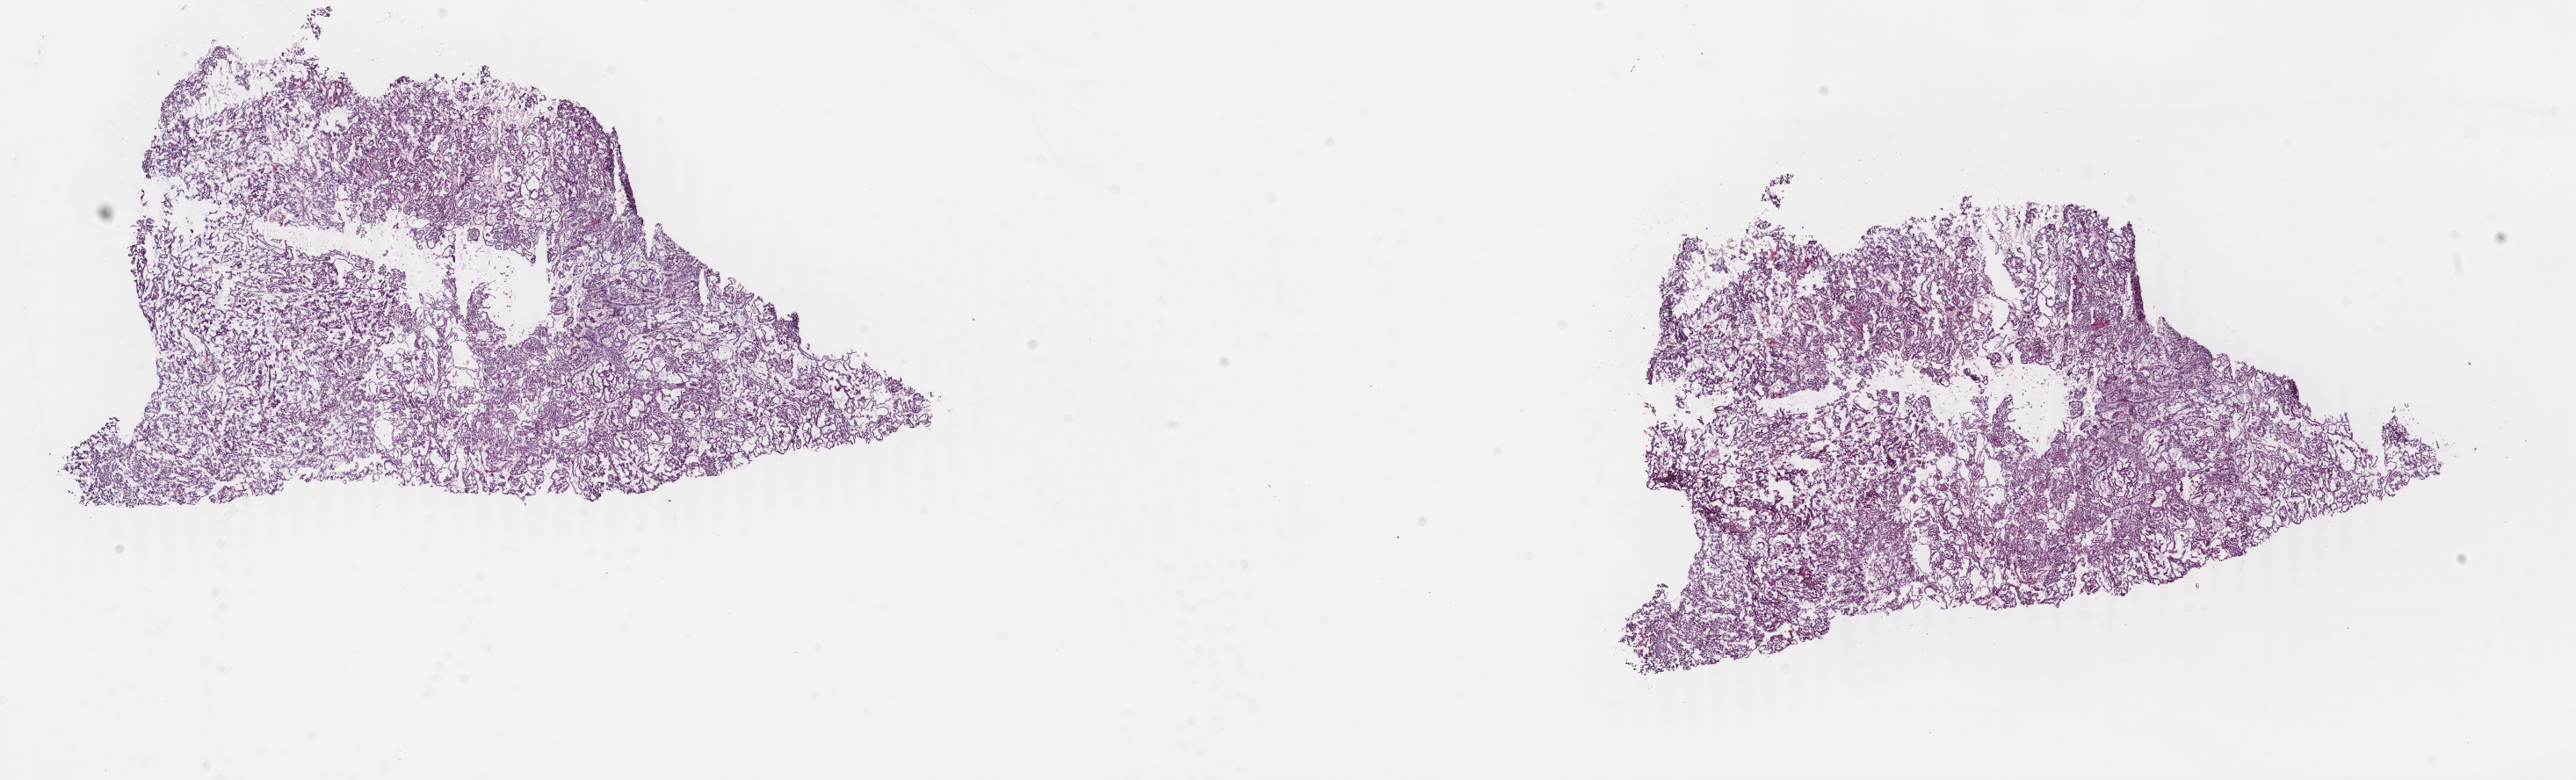
Digitized H&E tissue section (whole slide), a low-resolution overview of the entire scanned area, about 23.3 x 7.1 mm, frozen section from the top of the tissue portion, primary tumour sample from the kidney. Male, age 62 years at initial diagnosis. Pathologist review of this section (percent, as recorded): tumour cells 100%, tumour nuclei 80%, normal cells 0%, stromal cells 0%, necrosis 0%. Inflammatory infiltration, as recorded: lymphocyte infiltration 1%, monocyte infiltration 3%, neutrophil infiltration 0%.
AJCC pathologic stage: I (7th edition). Diagnosis: Papillary adenocarcinoma, NOS.